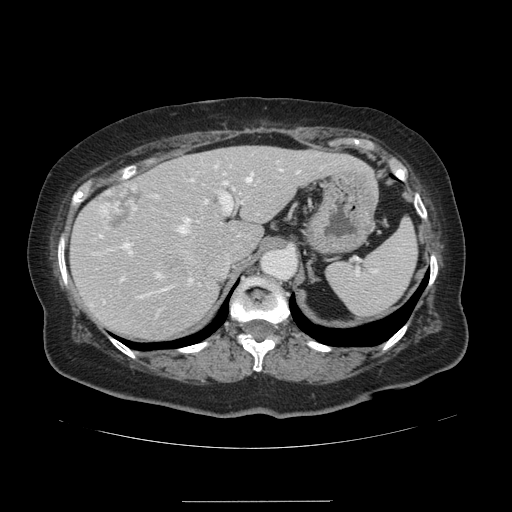
Contrast-enhanced abdominal CT, one axial slice; slice 91 of 141 in the series (ordered by position); intravenous contrast given; soft-tissue window (W 400 / L 40 HU); 2.5 mm slice thickness; 512 × 512 image matrix, field of view 393 × 393 mm. Female patient, age 74 years. From the clinical record (not read from this slice): diagnosis: colorectal cancer liver metastases, imaged before liver resection.
Structures marked on this image (expert manual segmentation):
- hepatic veins: bounding box [x1, y1, x2, y2] px = [99, 169, 281, 298]
- liver: [72, 147, 359, 339]
- planned liver remnant (the part of the liver to remain after resection): [72, 147, 359, 339]
- portal vein (with intrahepatic branches): [121, 165, 299, 280]
- liver metastasis: [100, 183, 140, 233]
- liver metastasis: [171, 263, 178, 268]